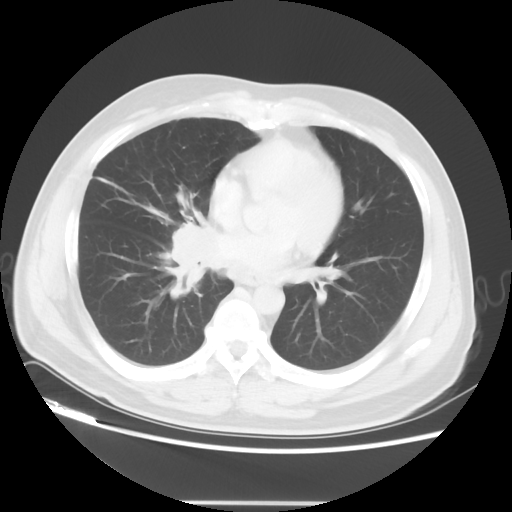
Chest CT, one axial slice. 120 kVp. Lung window (W 1500 / L -600 HU). 5 mm slice thickness. 512 × 512 image matrix, field of view 390 × 390 mm. Patient: male, 53 years. Case-level facts recorded for this patient, not image findings: clinical TNM (as recorded): T2 N3 M0.
Outlined on this slice (bounding box drawn by a radiologist):
- lung tumour (recorded histology: small cell carcinoma): box from (x=167, y=213) to (x=221, y=300) px